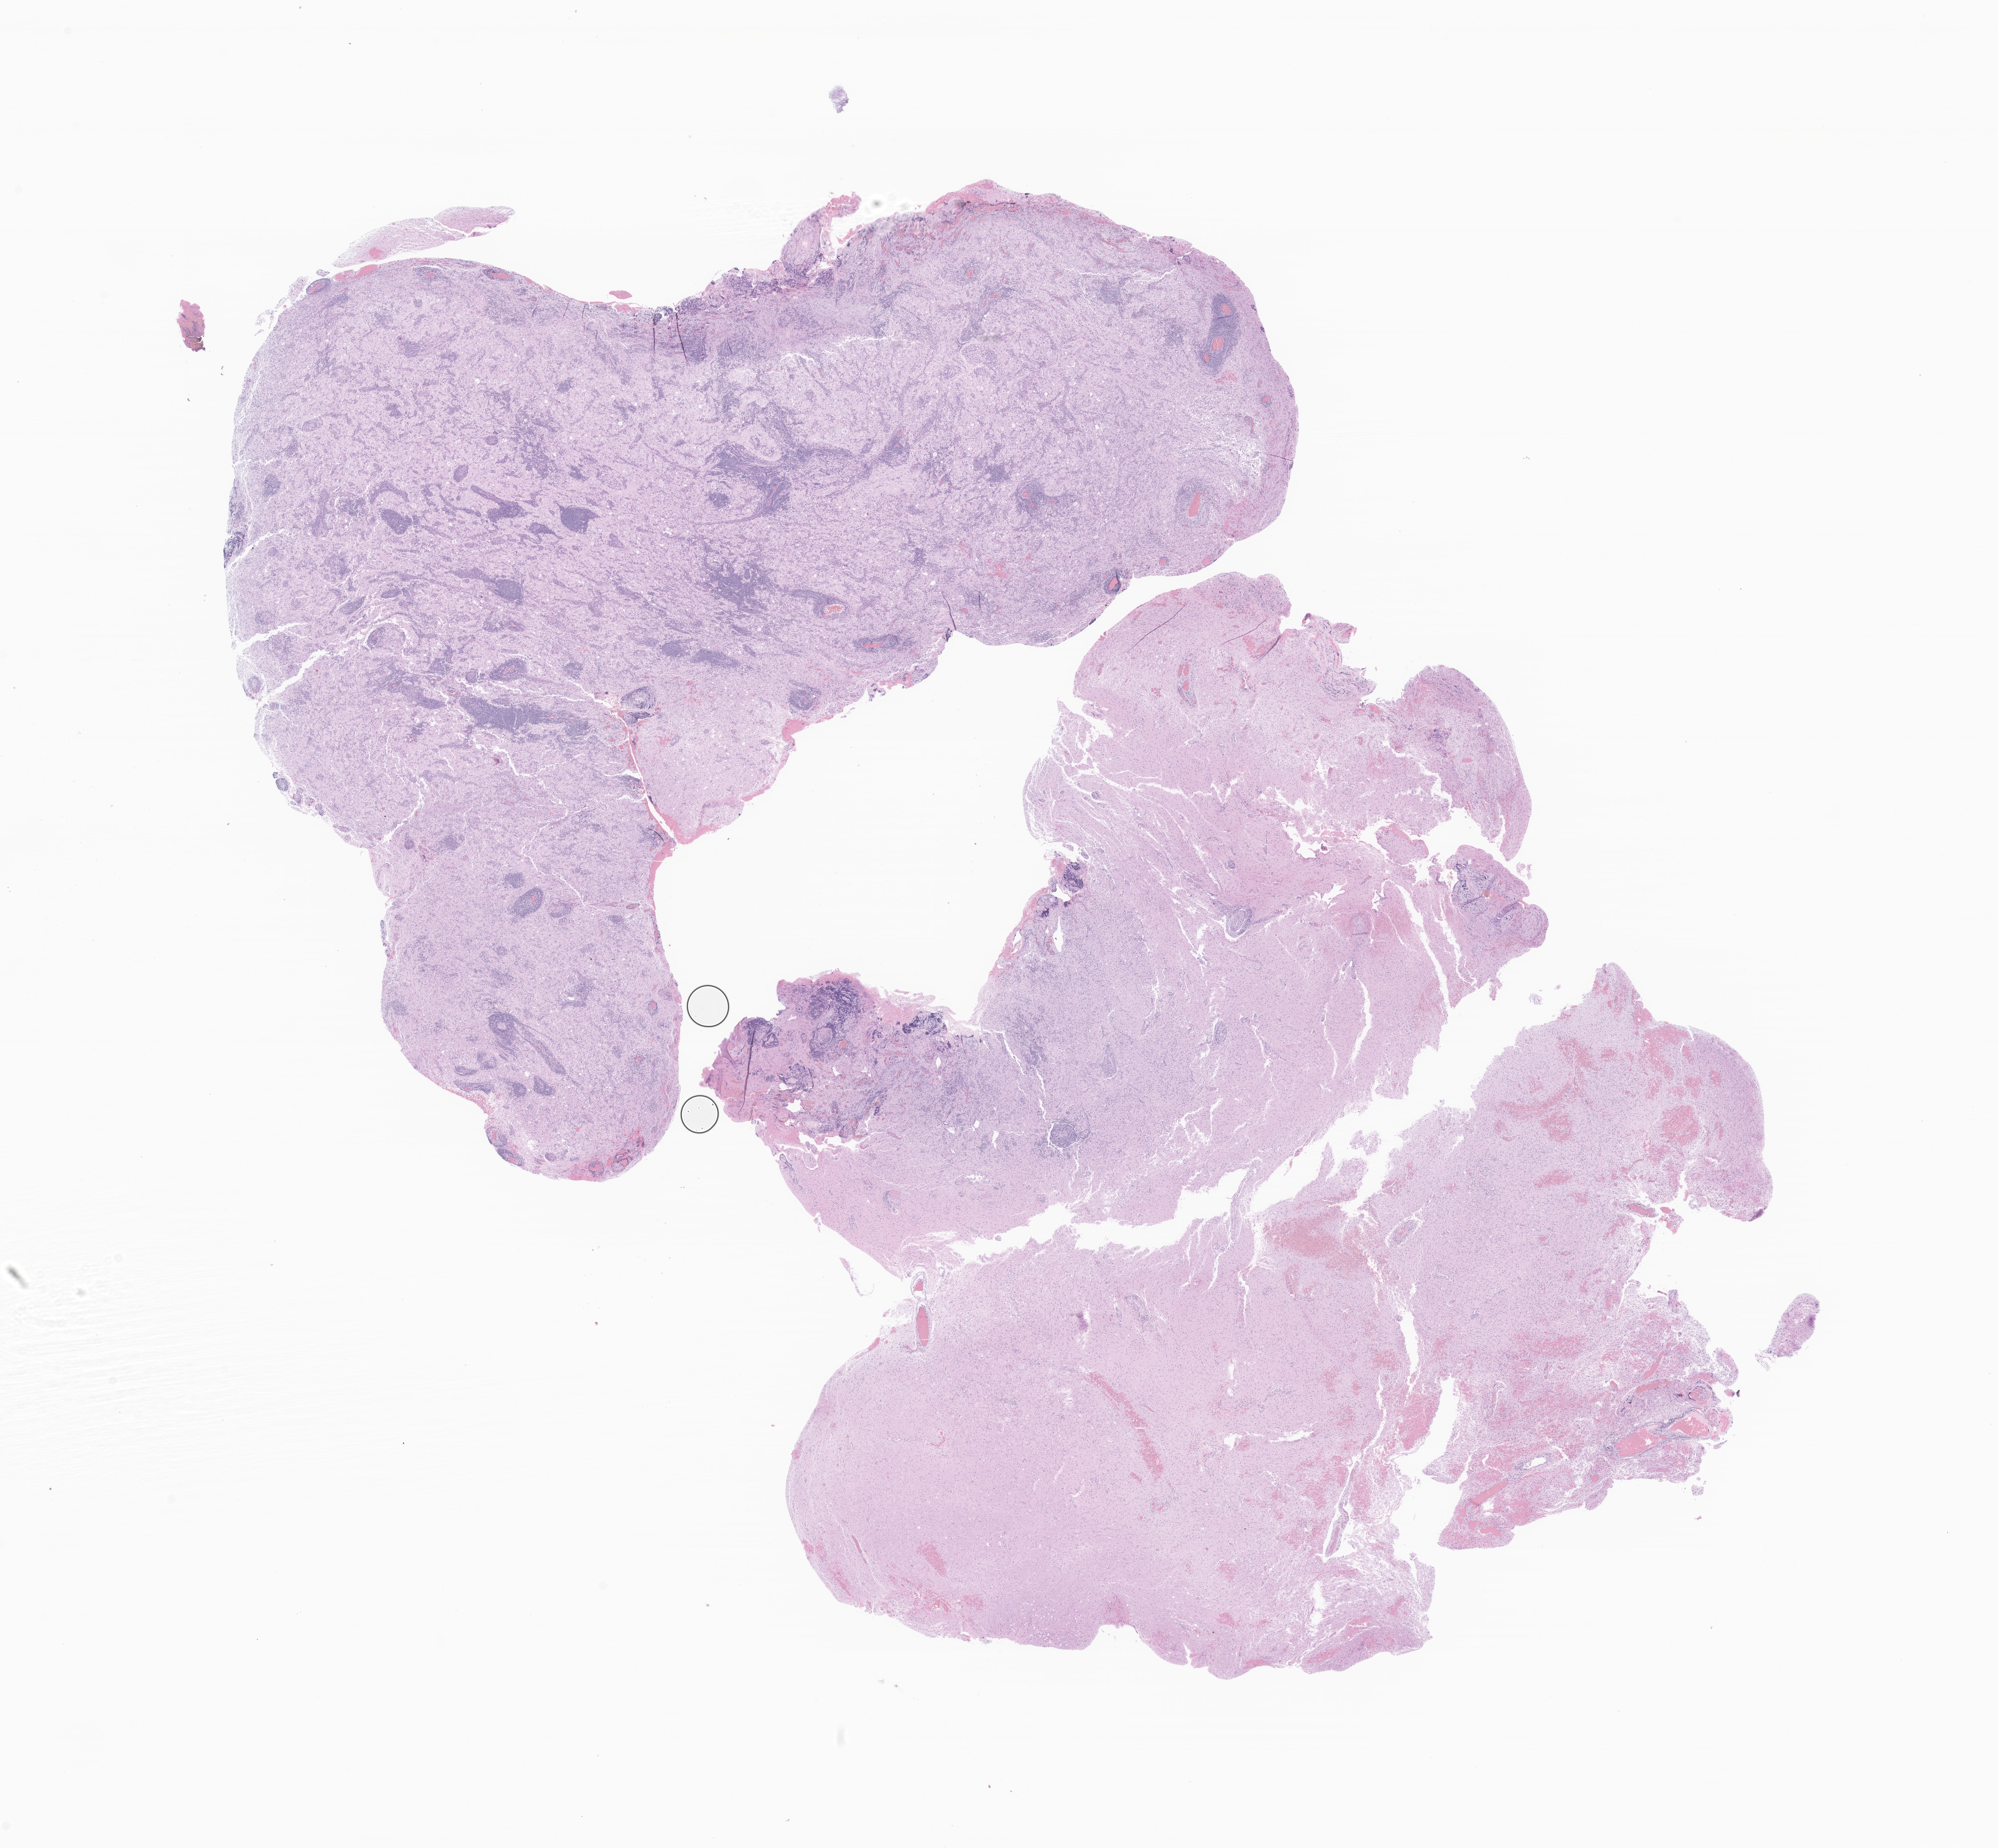
Digitized H&E-stained section of tumor tissue from the brain stem, low-resolution overview of the scanned area, about 21.1 x 19.5 mm; formalin-fixed, paraffin-embedded (FFPE) tissue. Patient: male, age 214 months (17 years 10 months).
Diagnosis (ICD-O-3 morphology term): Pilocytic astrocytoma.